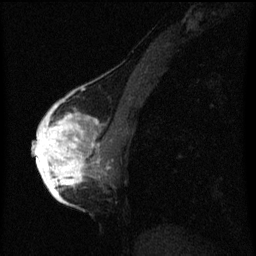
Breast MRI (dynamic contrast-enhanced), one sagittal slice; position 28 of 60 along the scan axis; dynamic contrast-enhanced series, image 2 of 3 at this slice position (ordered by acquisition); 1.5 T; TE 4.2 ms, TR 8 ms; 2 mm slice thickness; 256 × 256 image matrix. Patient: female, 56 years.
Annotated regions visible in this slice (semi-automatically segmented with operator editing):
- analysis volume of interest (the breast-tissue region the enhancement analysis was run in; not a lesion): bounding box (x1, y1, x2, y2) in pixels: (42, 110, 109, 193)
- tumour enhancement mask (voxels above the 70 % enhancement threshold inside the analysis volume of interest): (42, 110, 99, 193)